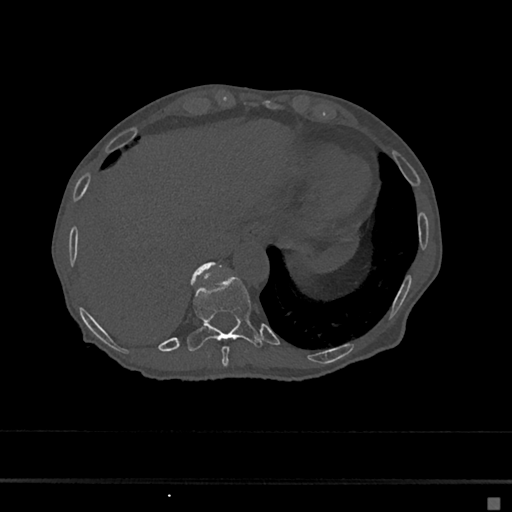
CT including the spine, one axial slice; slice 229 of 797 in the series (ordered by position); 120 kVp; bone window (W 1800 / L 400 HU); 512 × 512 image matrix, field of view 360 × 360 mm. Patient: female, 68 years. From the clinical record (not read from this slice): primary cancer: renal.
Annotated regions visible in this slice (semi-automatic segmentation, software-assisted and operator-edited):
- T10 vertebra: bounding box <188,276,261,351> (left, top, right, bottom; pixels)
- T11 vertebra: <192,262,220,279>
- T9 vertebra: <221,346,230,366>